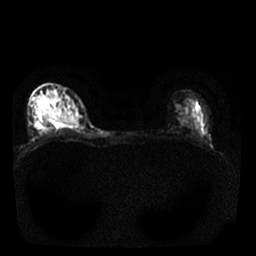
Breast MRI, one axial slice. Position 16 of 25 along the scan axis. Diffusion-weighted series; image 2 of 4 stored at this slice position (different b-values; order by instance number). 1.5 T. 256 × 256 image matrix, field of view 310 × 310 mm. Female patient.
Annotated regions visible in this slice (manually delineated by an expert):
- tumour on diffusion-weighted imaging: bounding box <42,105,78,126> (left, top, right, bottom; pixels)